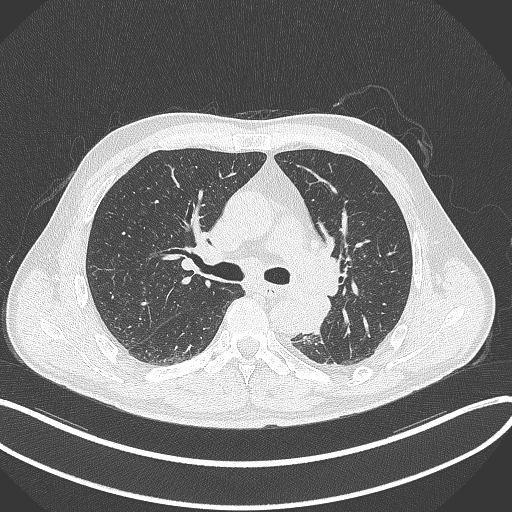
Chest CT, one axial slice; slice 213 of 329 in the series (ordered by position); 120 kVp; lung window (W 1500 / L -600 HU); 512 × 512 image matrix. Patient: male, 59 years. From the clinical record (not read from this slice): clinical TNM (as recorded): T2a N2 M0.
Structures marked on this image (bounding box drawn by a radiologist):
- lung tumour (recorded histology: squamous cell carcinoma): bounding box <300,295,333,337> (left, top, right, bottom; pixels)